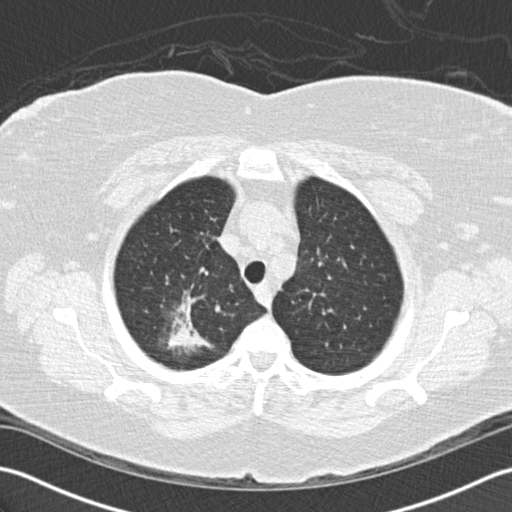
Chest CT (low-dose screening protocol), one axial image, baseline screening round, lung window (W 1500 / L -600 HU), 2 mm slice thickness, 120 kVp, slice 26 of 156 in the series. Female, age 72 years at enrolment.
Expert reader's lesion annotation, bounding box (x1, y1, x2, y2) in pixels: (137, 275, 230, 367). The screening reader recorded 2 non-calcified nodules or masses ≥4 mm on this exam (right lower lobe, right lower lobe); which of them this box marks is not recorded. Official screen result: positive, change unspecified: nodule(s) >= 4 mm or enlarging nodule(s), mass(es), or other non-specific abnormalities suspicious for lung cancer. Lung cancer was diagnosed 494 days after this screen (after the second annual screen): bronchiolo-alveolar adenocarcinoma, NOS, right upper lobe, stage IIIB (AJCC 6th edition), 45 mm at pathology.